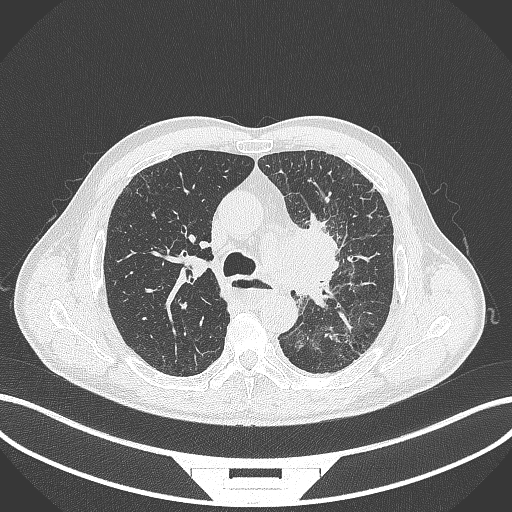
Chest CT, one axial slice. Position 257 of 411 along the scan axis. Lung window (W 1500 / L -600 HU). 512 × 512 image matrix, field of view 400 × 400 mm. Male patient, age 57 years. From the clinical record (not read from this slice): clinical TNM (as recorded): T2a N1 M0.
Annotated regions visible in this slice (rectangle marked by the reading radiologist):
- lung tumour (recorded histology: squamous cell carcinoma): box from (x=285, y=216) to (x=344, y=311) px